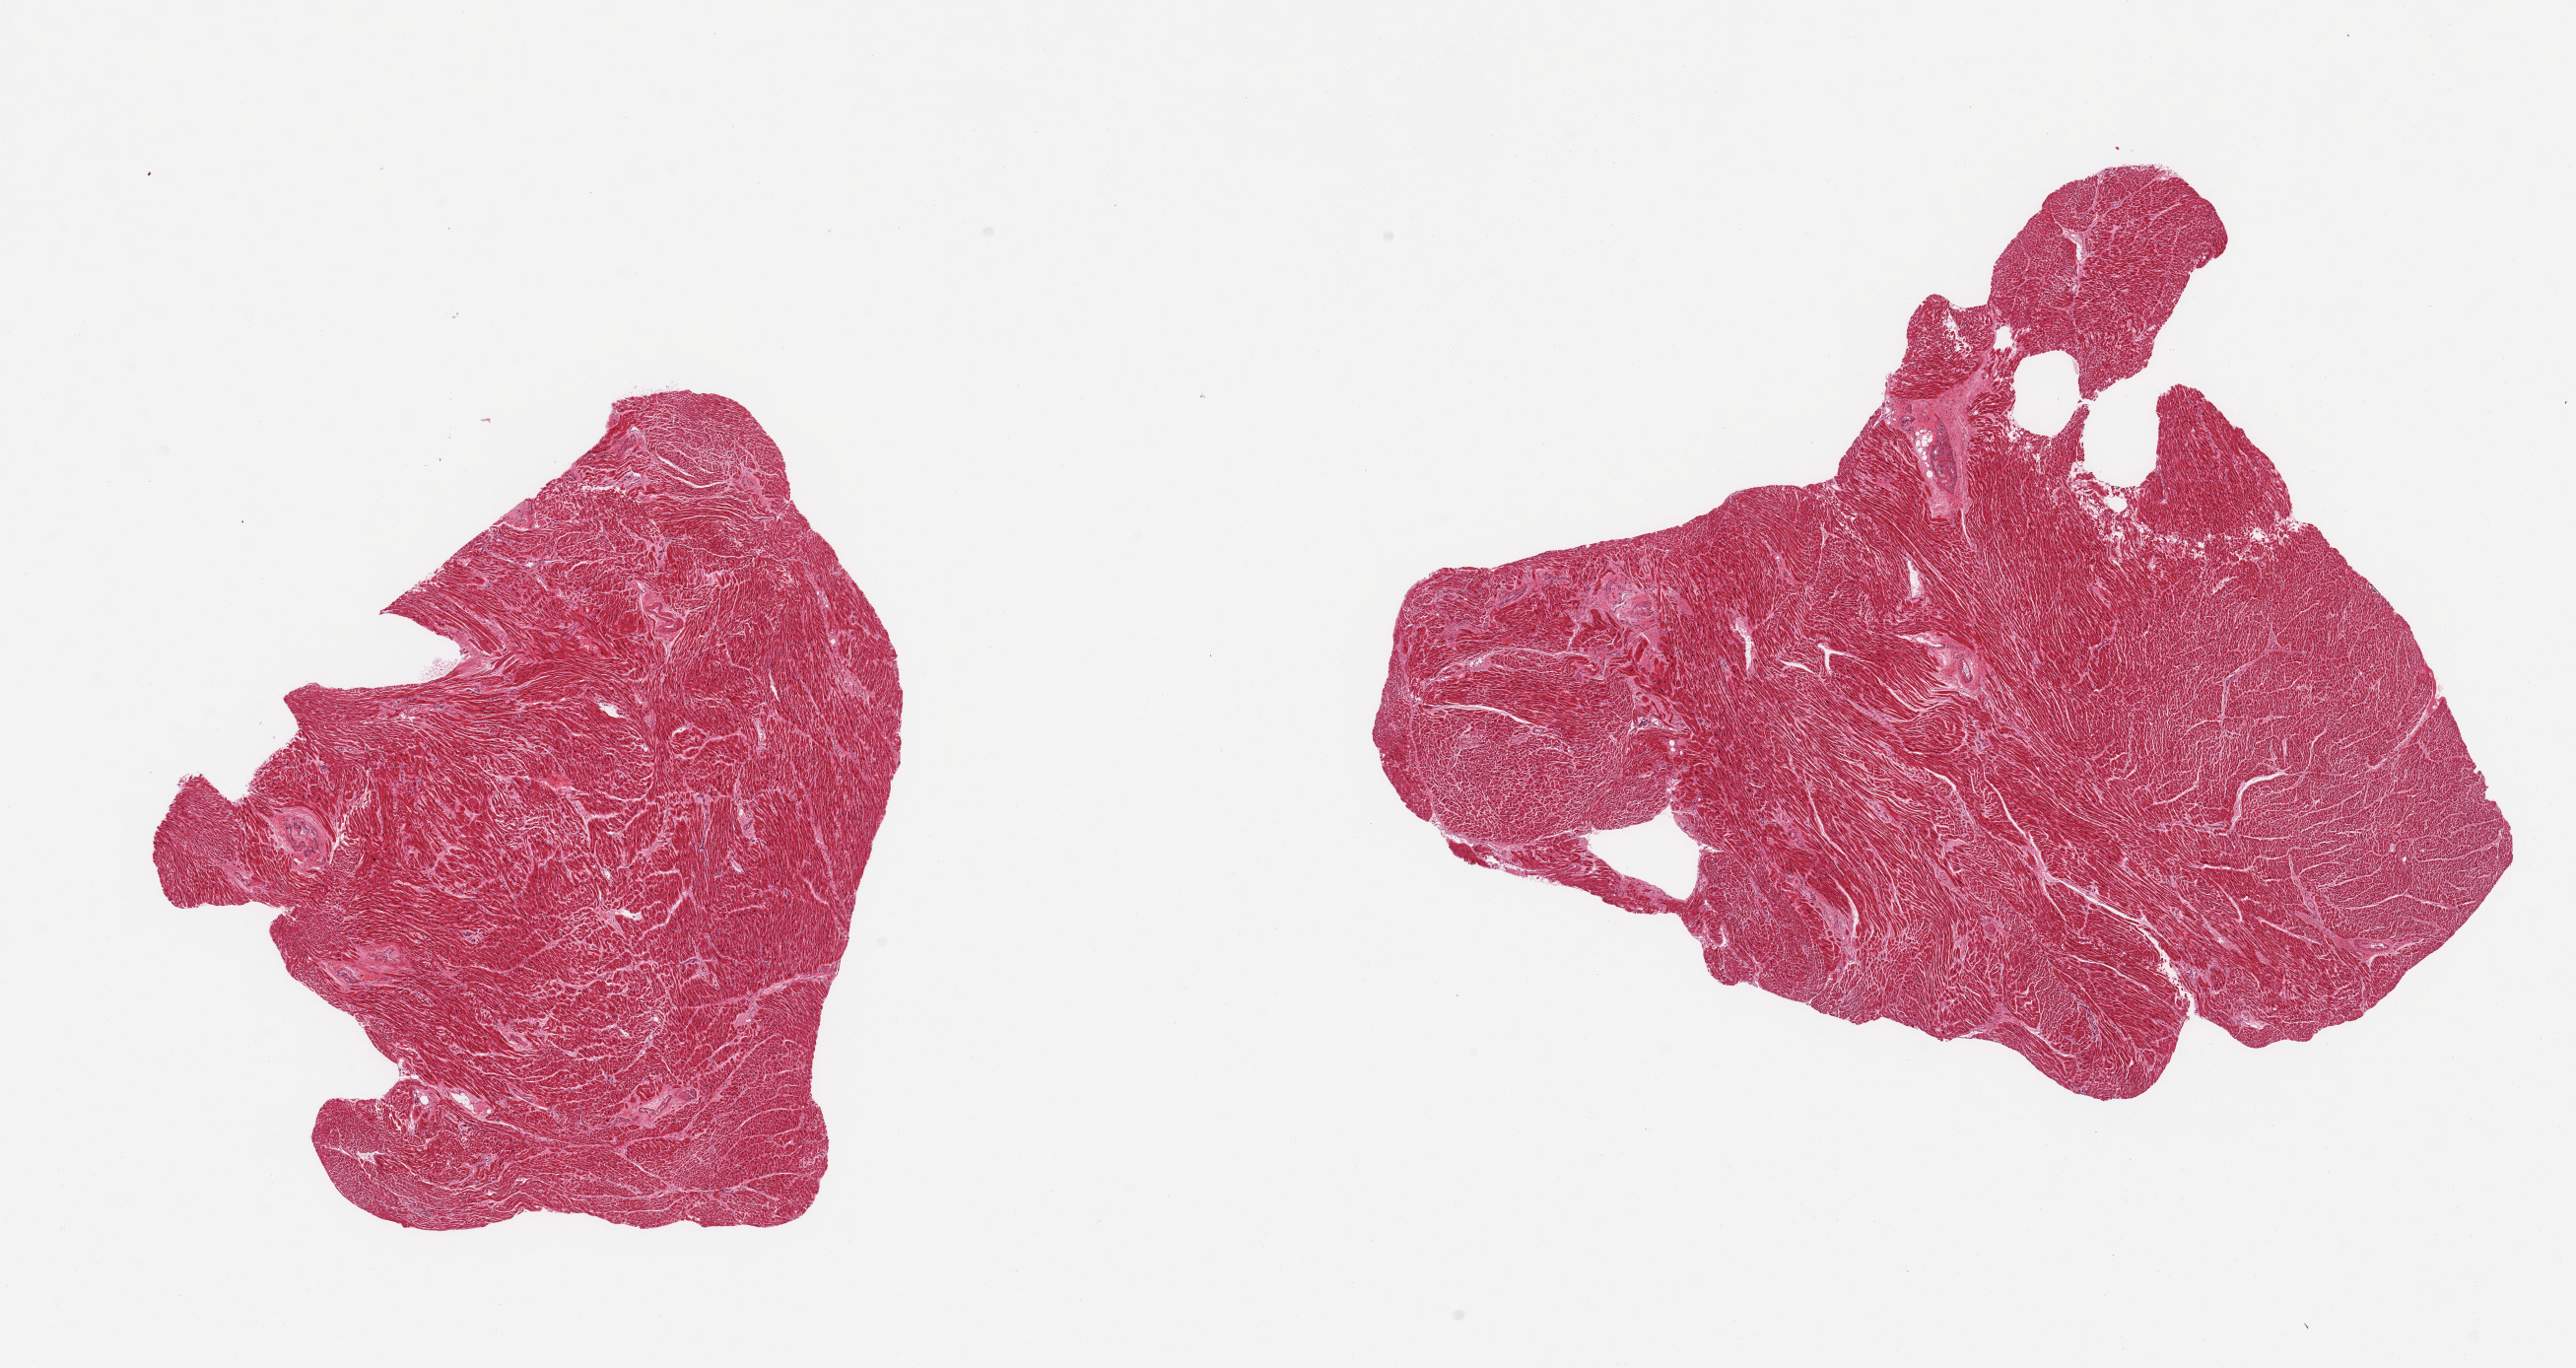
Whole-slide image, haematoxylin and eosin stain — low-resolution overview of the scanned area, about 20.7 x 11.0 mm (from a 20x scan); PAXgene-fixed paraffin-embedded (PFPE) section; target tissue: heart; donor tissue sample. Female donor.
Reviewer comment on this tissue sample: 2 pieces; no lesions; minimal fibrous content.